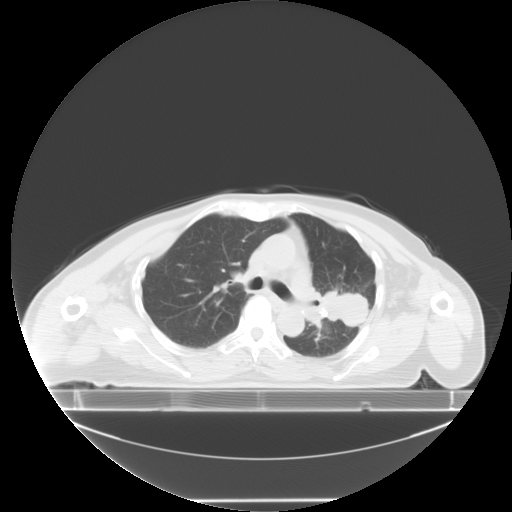
Chest CT, one axial slice. Position 5 of 24 along the scan axis. Reconstruction kernel STANDARD. 120 kVp. Lung window (W 1500 / L -600 HU). 5 mm slice thickness. 512 × 512 image matrix, field of view 500 × 500 mm. Female patient, age 74 years. From the clinical record (not read from this slice): clinical TNM (as recorded): T3 N1 M1c; histopathological grade: G3.
Structures marked on this image (bounding box drawn by a radiologist):
- lung tumour (recorded histology: small cell carcinoma): bounding box <311,279,375,330> (left, top, right, bottom; pixels)